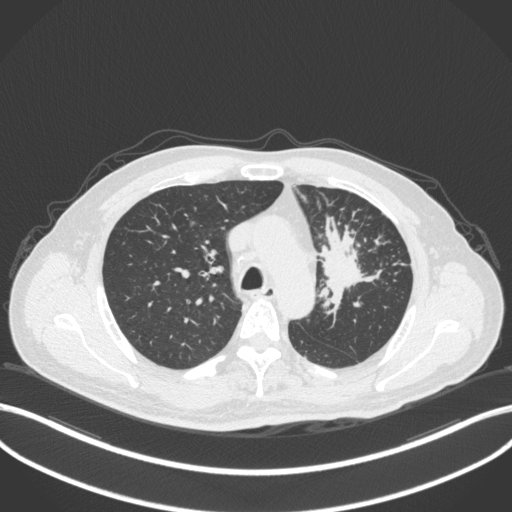
Chest CT, one axial slice; reconstruction kernel B31f; 120 kVp; lung window (W 1500 / L -600 HU); 1 mm slice thickness; 512 × 512 image matrix, field of view 400 × 400 mm. Patient: male, 69 years. Case-level facts recorded for this patient, not image findings: clinical TNM (as recorded): T2a N2 M0.
Annotated regions visible in this slice (bounding box drawn by a radiologist):
- lung tumour (recorded histology: adenocarcinoma): bounding box <312,214,383,309> (left, top, right, bottom; pixels)